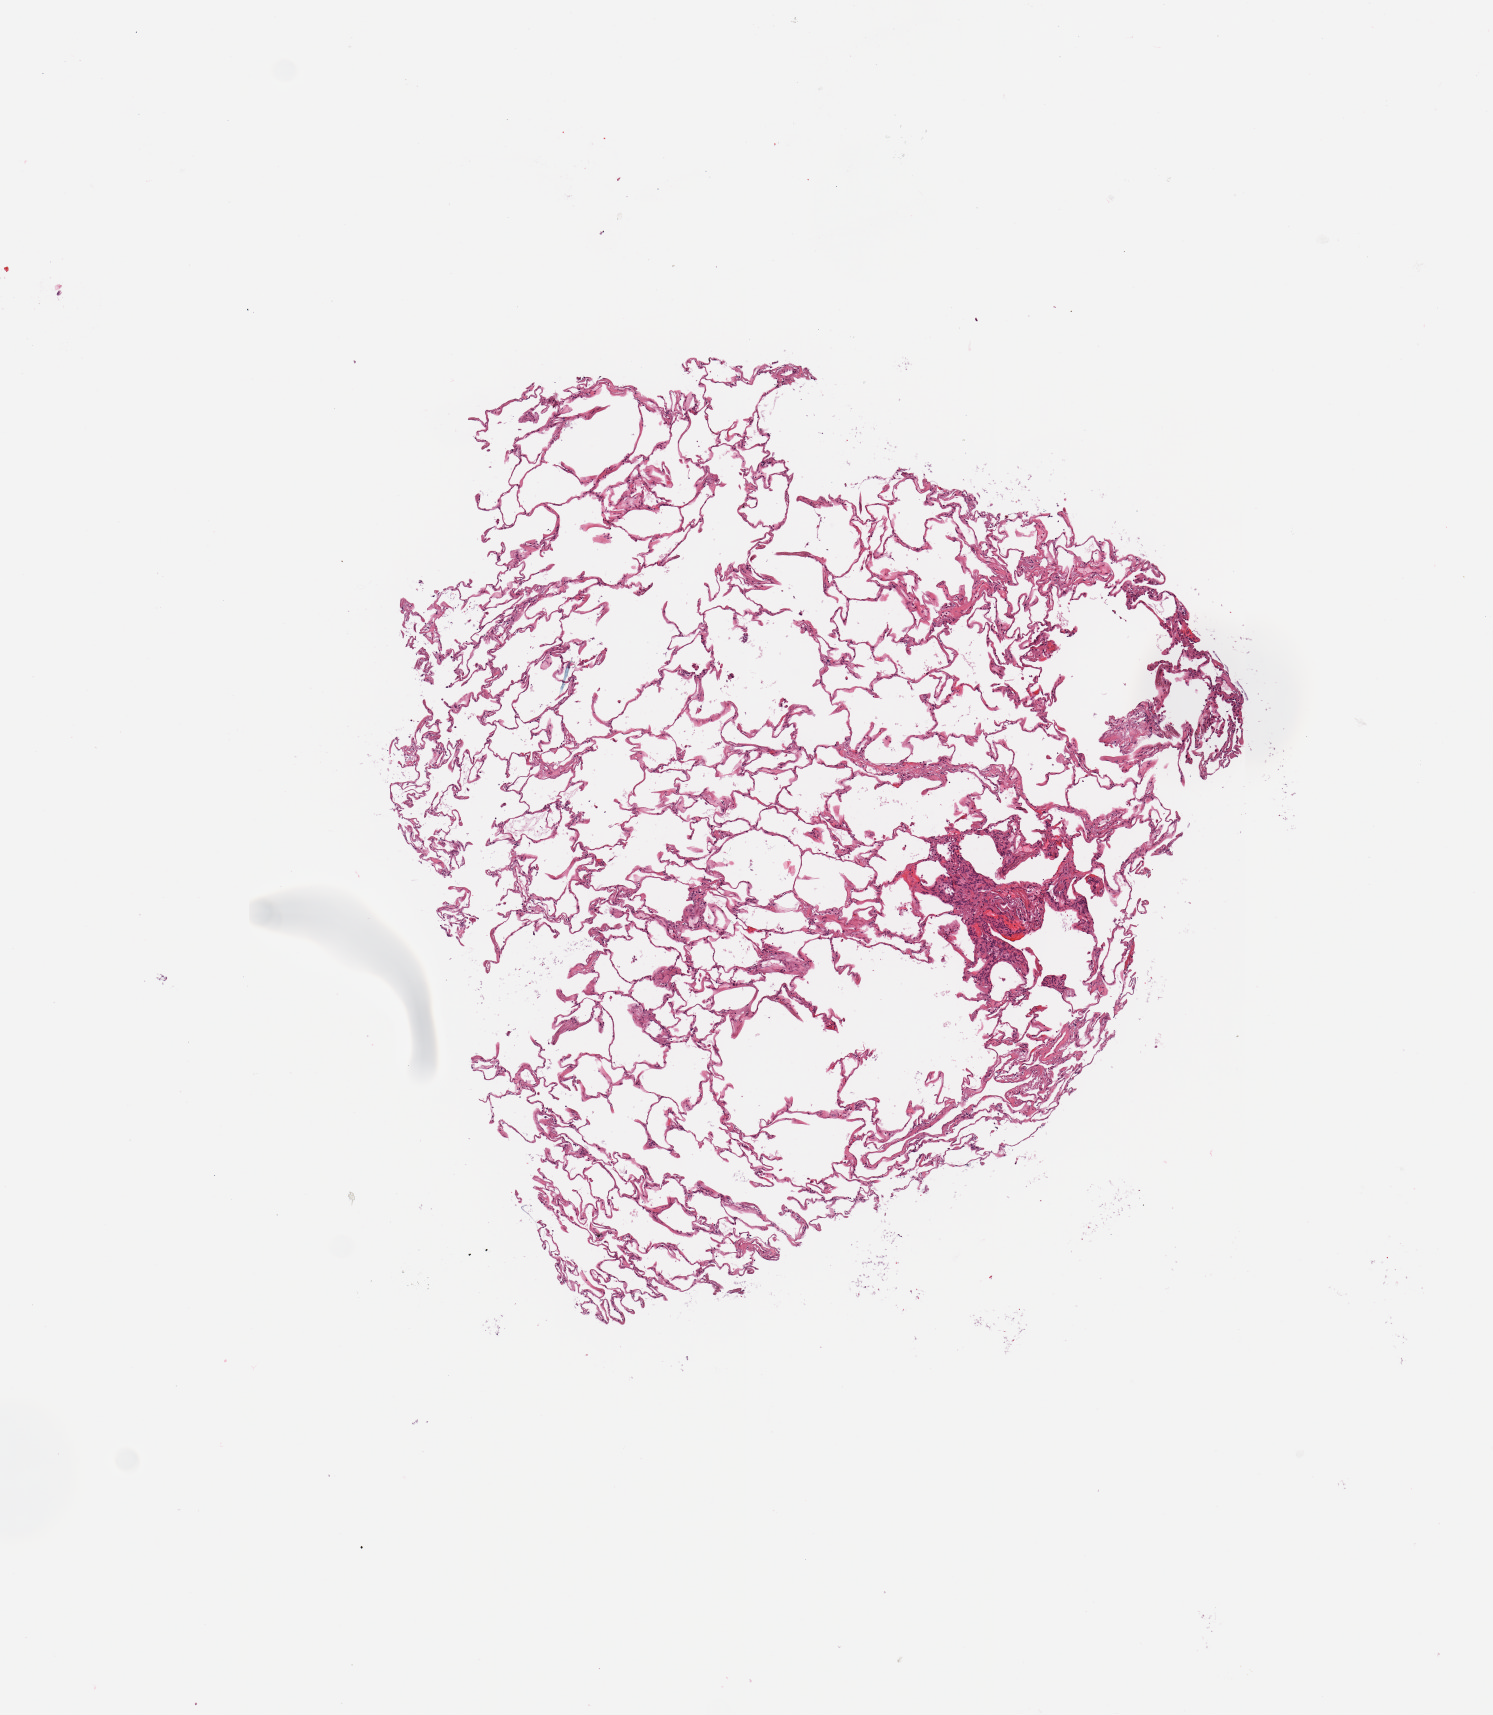
Digitized Hematoxylin and eosin (H&E) stained tissue section (whole slide), low-resolution overview of the scanned area, about 5.9 x 6.8 mm (acquisition: 20x scan). Normal (non-tumour) tissue sample, sampled site: lung. 68-year-old female patient.
This section: normal (non-tumour) tissue from the same patient. Patient diagnosis: Adenocarcinoma, NOS.